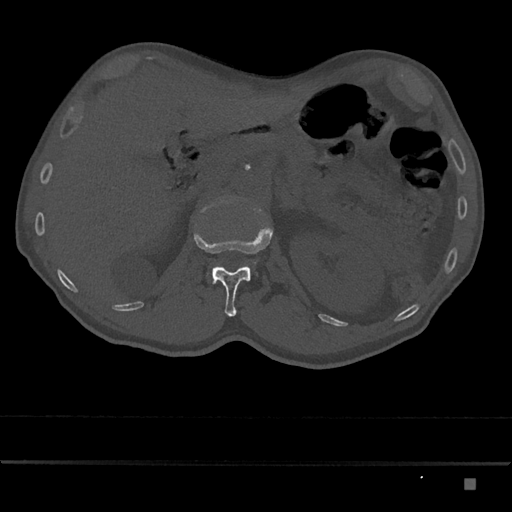
CT including the spine, one axial slice; slice 529 of 797 in the series (ordered by position); reconstruction kernel Br40s/3; 120 kVp; bone window (W 1800 / L 400 HU); 0.5 mm slice thickness; 512 × 512 image matrix, field of view 390 × 390 mm. Patient: male, 72 years. Case-level facts recorded for this patient, not image findings: primary cancer: prostate.
Outlined on this slice (semi-automatically segmented with operator editing):
- L1 vertebra: box from (x=194, y=225) to (x=273, y=317) px
- L2 vertebra: (x=207, y=262)–(x=256, y=275)